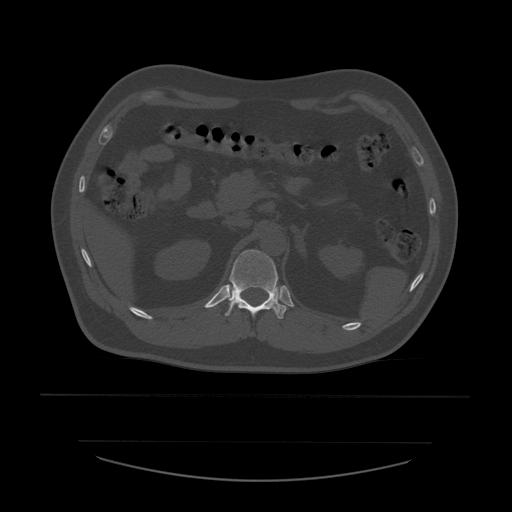
CT including the spine, one axial slice; position 250 of 532 along the scan axis; reconstruction kernel STANDARD; 120 kVp; bone window (W 1800 / L 400 HU); 1.25 mm slice thickness; 512 × 512 image matrix, field of view 441 × 441 mm. Patient age 44 years. From the clinical record (not read from this slice): primary cancer: soft tissue sarcoma.
Structures marked on this image (semi-automatic segmentation, software-assisted and operator-edited):
- T12 vertebra: box from (x=225, y=250) to (x=287, y=319) px